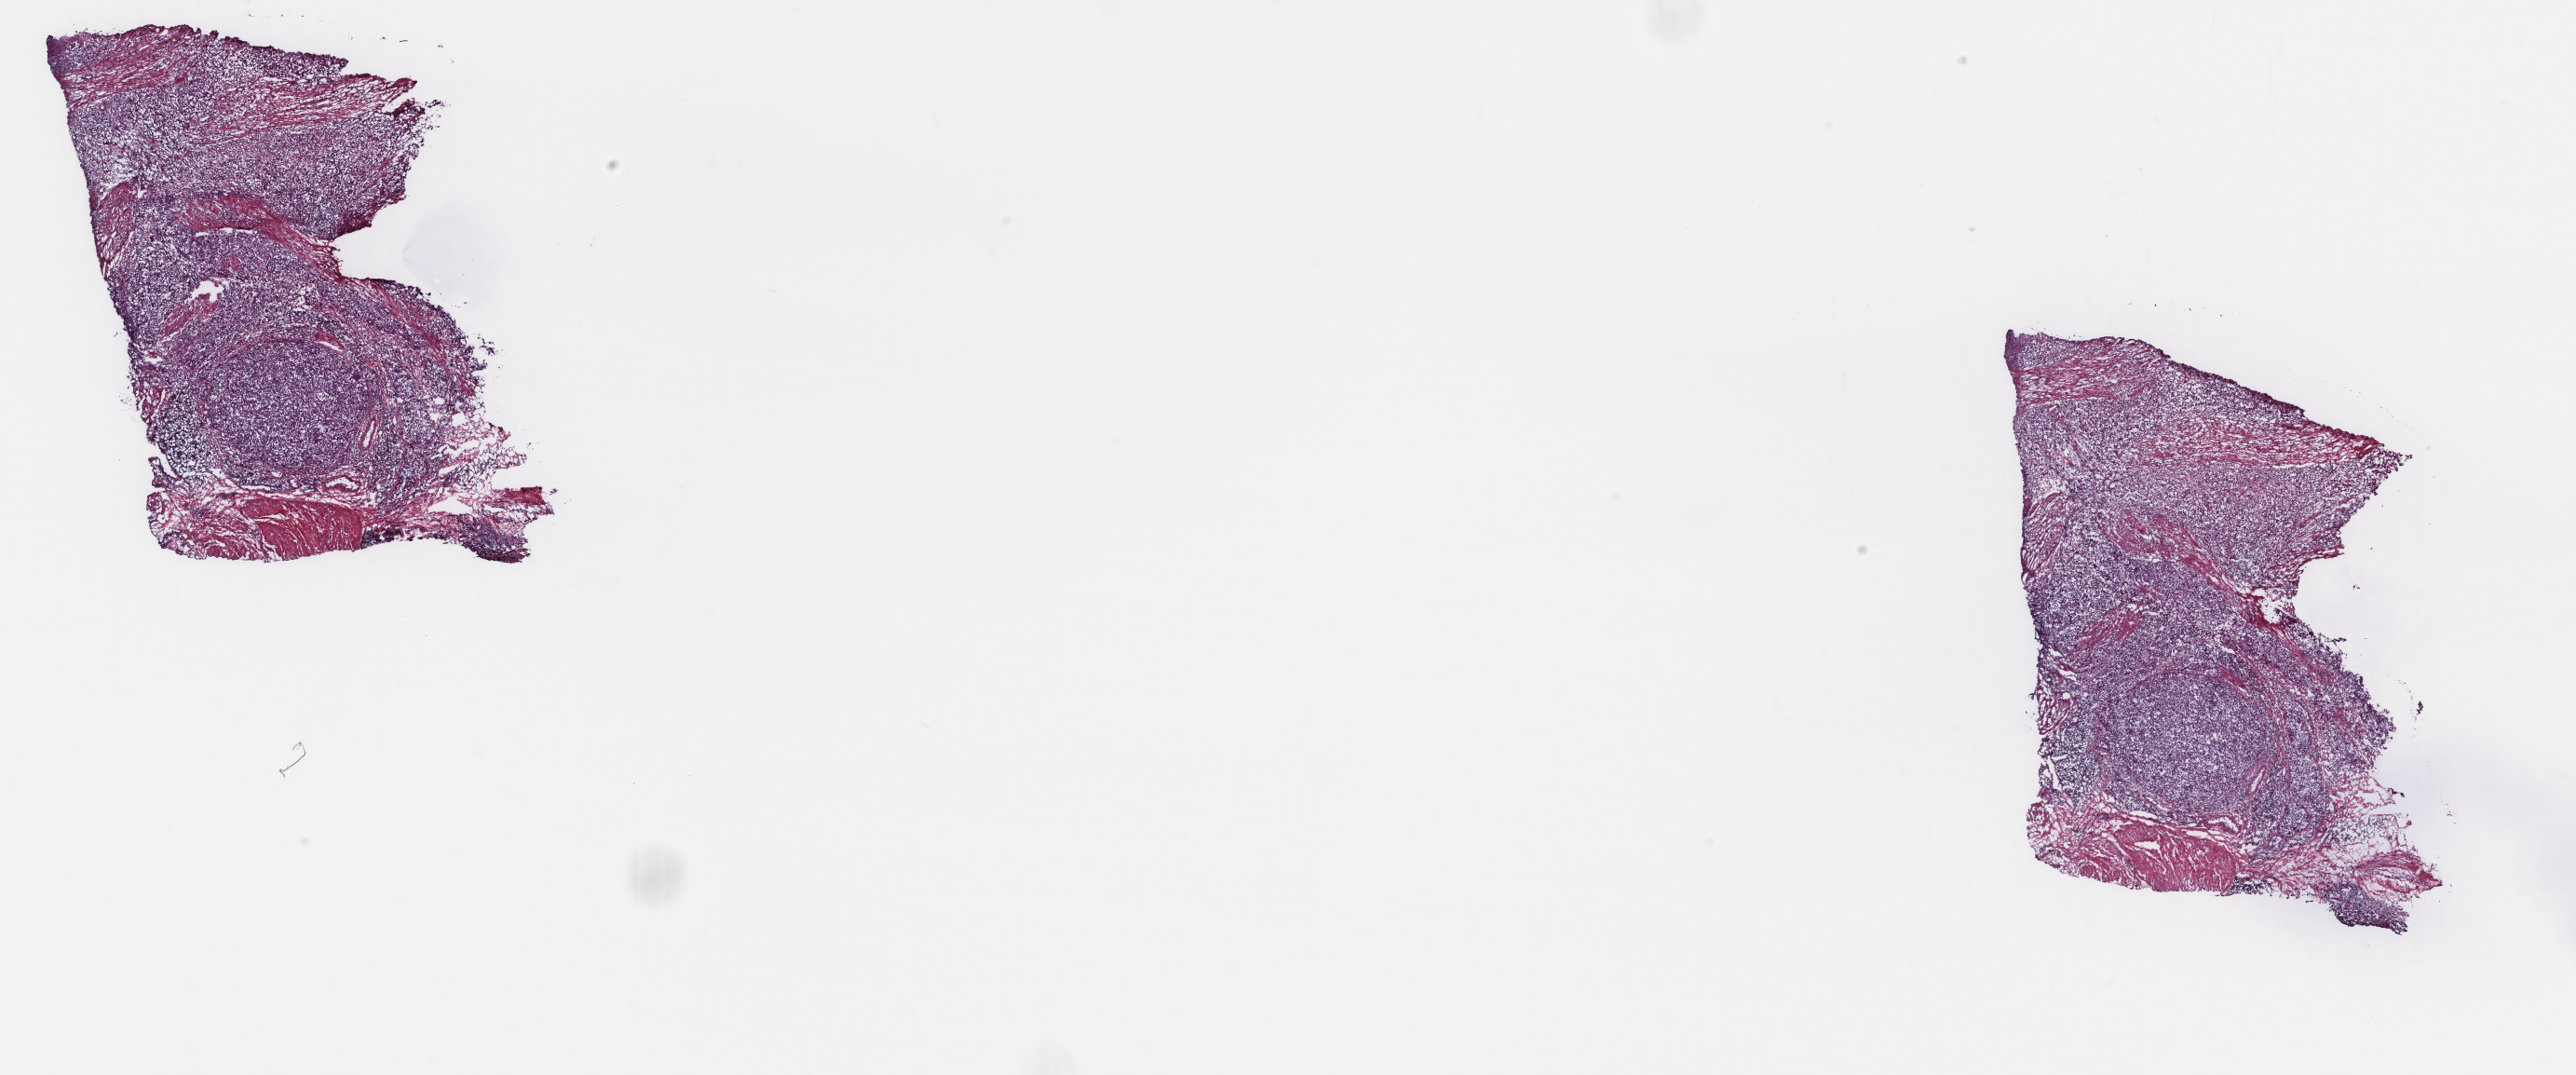
Whole-slide histology image, H&E-stained — shown as a low-resolution overview of the whole scanned area (about 22.0 x 9.2 mm), frozen section from the top of the tissue portion, primary tumour sample from the bladder. Male, age 58 years at initial diagnosis. Histologic grade: high grade. Slide review estimates, as recorded: tumour cells 75%, tumour nuclei 90%, normal cells 25%, stromal cells 0%, necrosis 0%. Inflammatory infiltration, as recorded: lymphocyte infiltration 5%, monocyte infiltration 0%, neutrophil infiltration 0%.
AJCC pathologic stage: II (6th edition). Pathologic diagnosis: Transitional cell carcinoma.